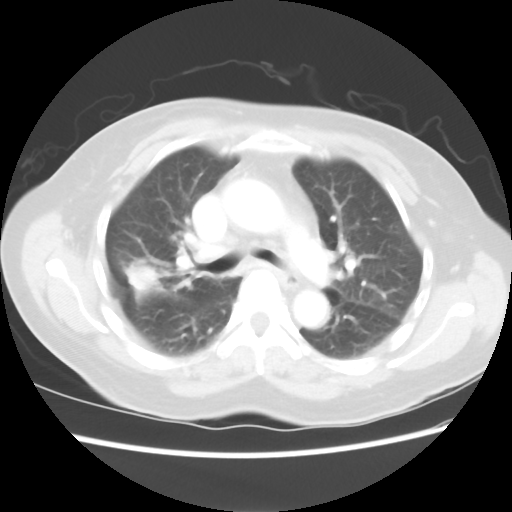
Chest CT, one axial slice. Slice 45 of 80 in the series (ordered by position). 100 kVp. Lung window (W 1500 / L -600 HU). 5 mm slice thickness. 512 × 512 image matrix, field of view 342 × 342 mm. Female patient, age 67 years. Case-level facts recorded for this patient, not image findings: clinical TNM (as recorded): T1c N1 M0.
Structures marked on this image (rectangle marked by the reading radiologist):
- lung tumour (recorded histology: adenocarcinoma): bounding box <116,245,171,306> (left, top, right, bottom; pixels)